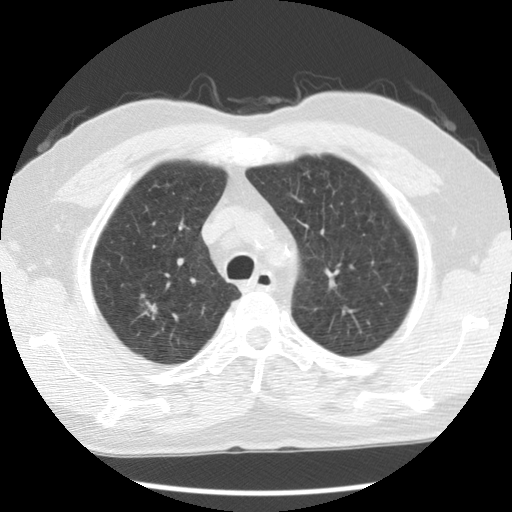
Axial slice from a low-dose chest CT screening exam, baseline screening round, lung window (W 1500 / L -600 HU), slice 87 of 110 in the series. Male, age 68 years at enrolment. Former smoker at enrolment.
• Expert-annotated lung lesion, bounding box (x1, y1, x2, y2) in pixels: (132, 293, 169, 329).
• The exam's reader record, not a measurement of the box and not confirmed to be the same lesion: non-calcified nodule or mass ≥4 mm, right upper lobe, 9 × 7 mm, poorly defined margins, ground glass attenuation.
• Lung cancer was diagnosed 410 days after this screen (after the second annual screen): adenocarcinoma, NOS, right upper lobe, moderately differentiated (G2), stage IA (AJCC 6th edition), 28 mm at pathology.